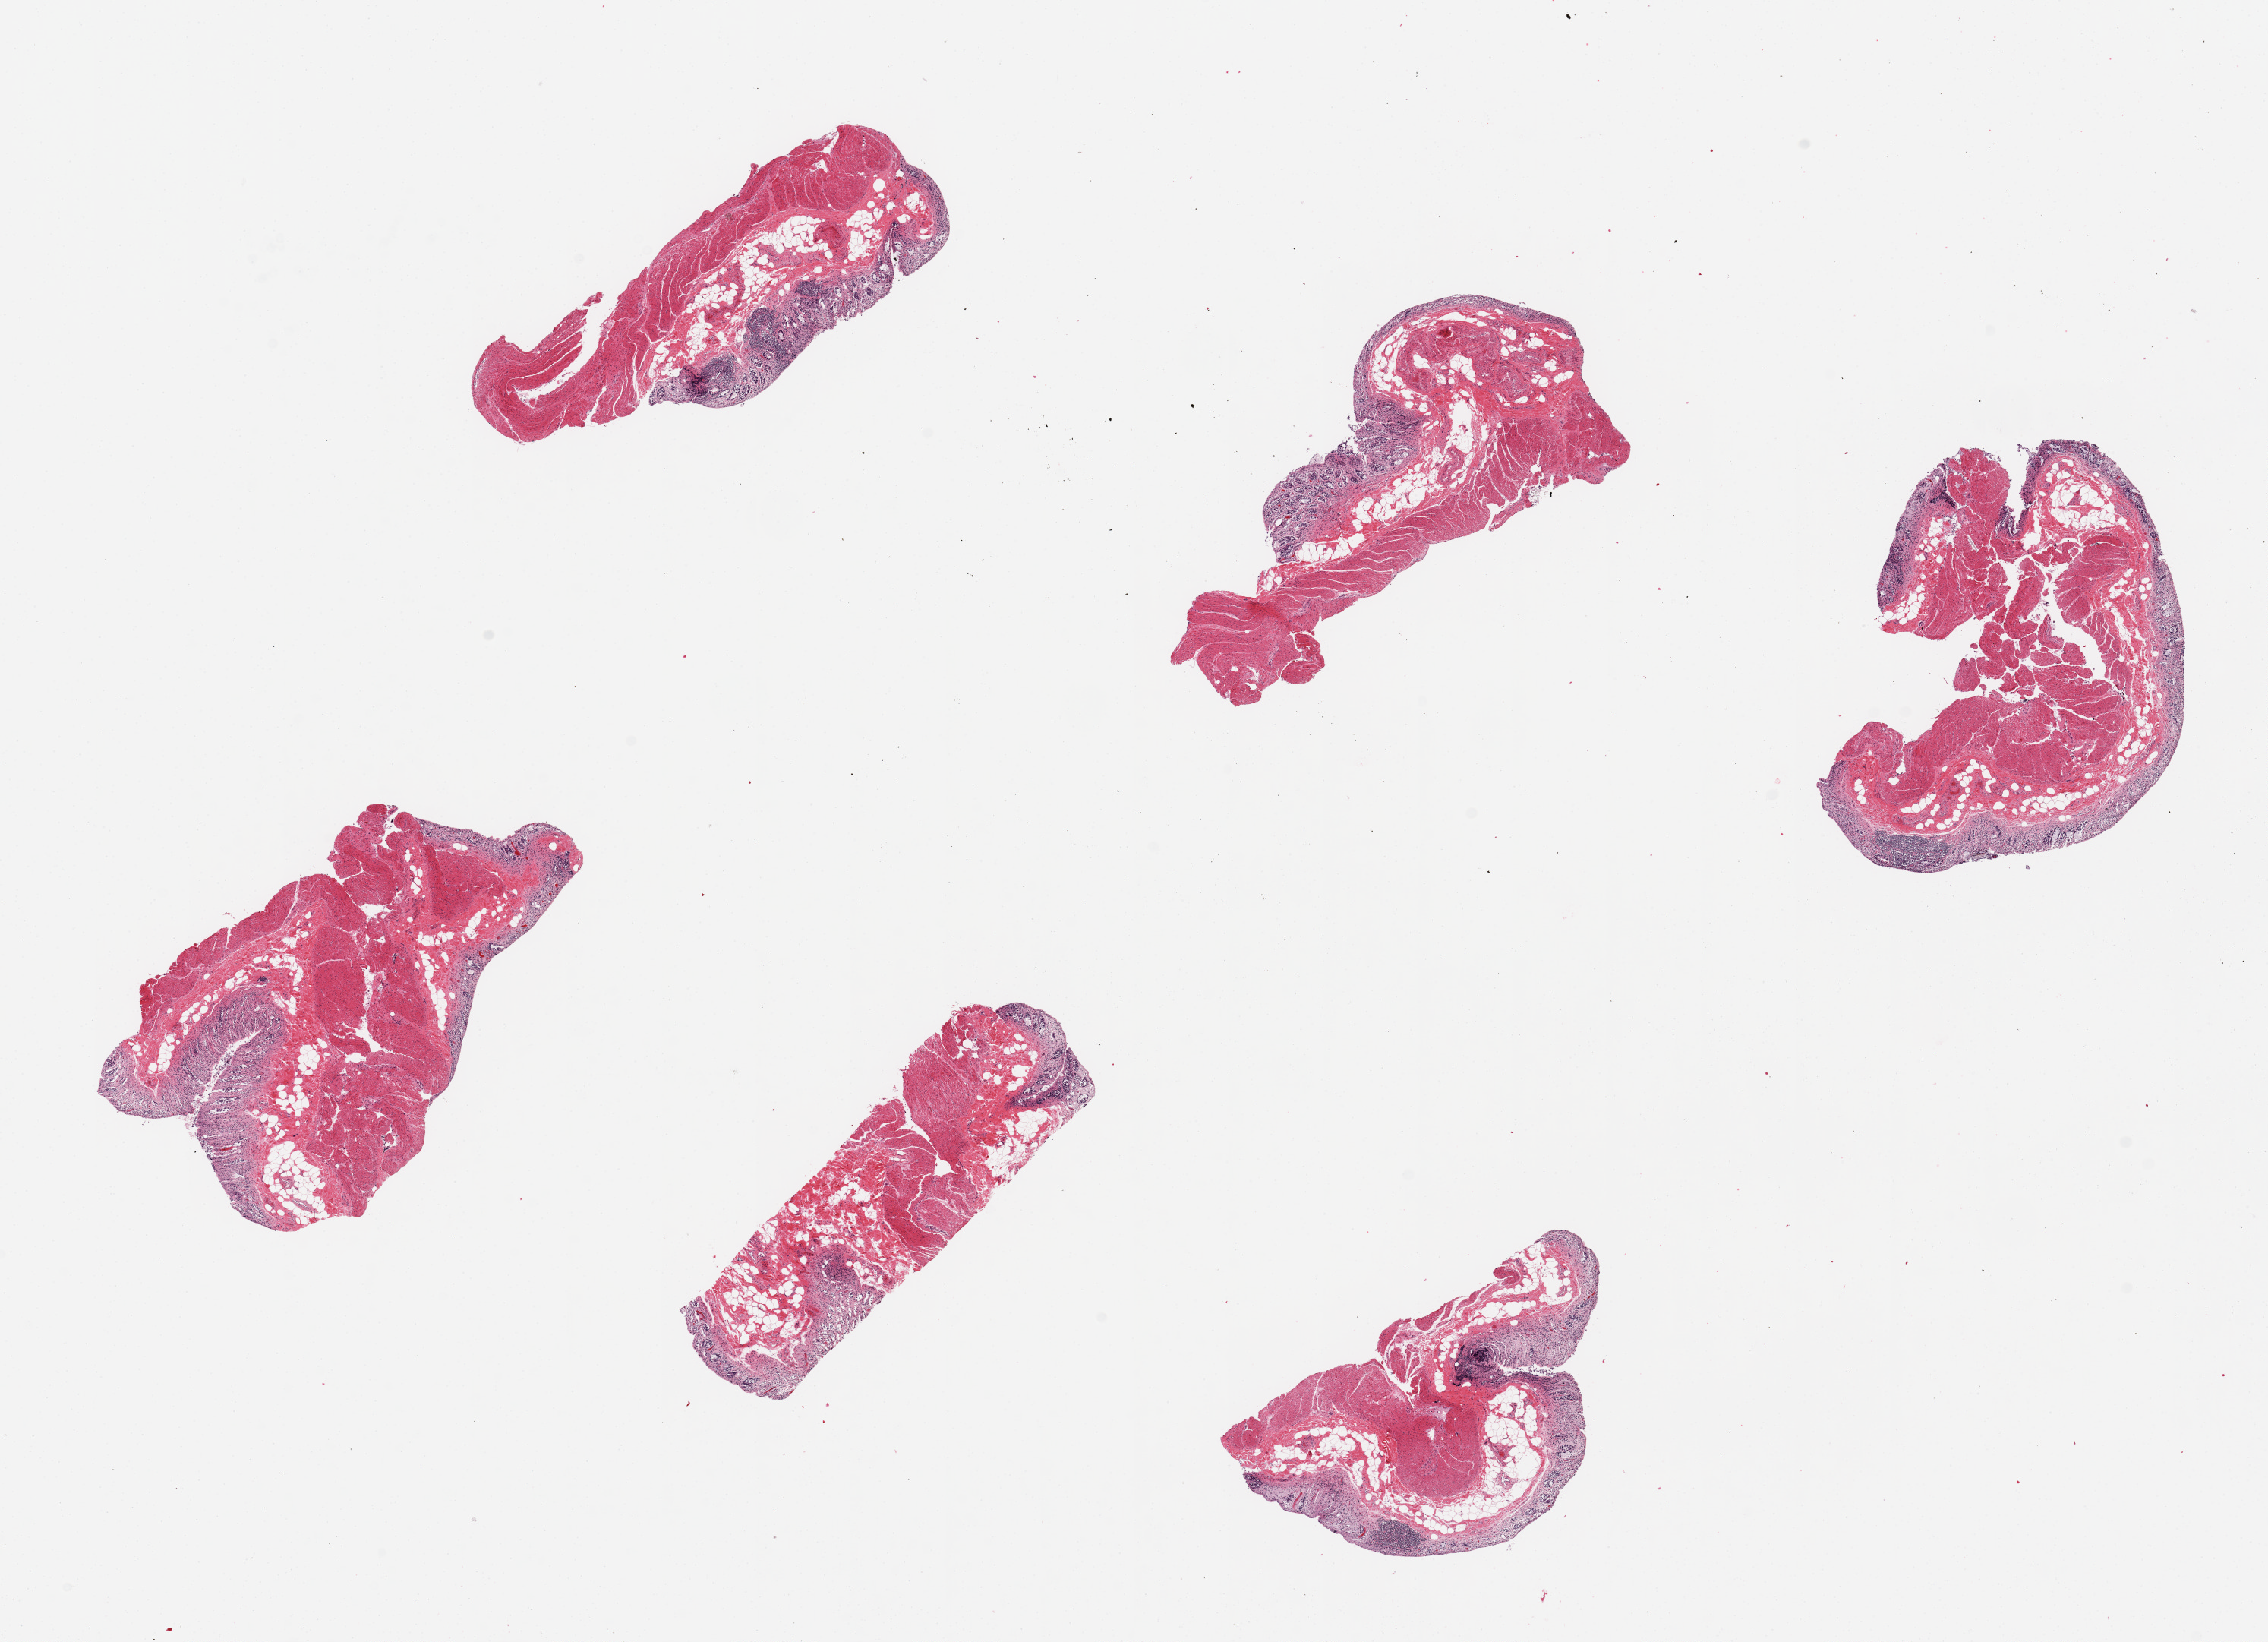
Whole-slide image, haematoxylin and eosin stain, shown as a low-resolution overview of the whole scanned area (about 23.6 x 17.1 mm), PAXgene-fixed paraffin-embedded (PFPE) section, sampled site (target tissue): transverse colon, donor tissue sample.
* pathologist's review note for this sample: 6 pieces; autolyzed mucosa and preserved muscularis